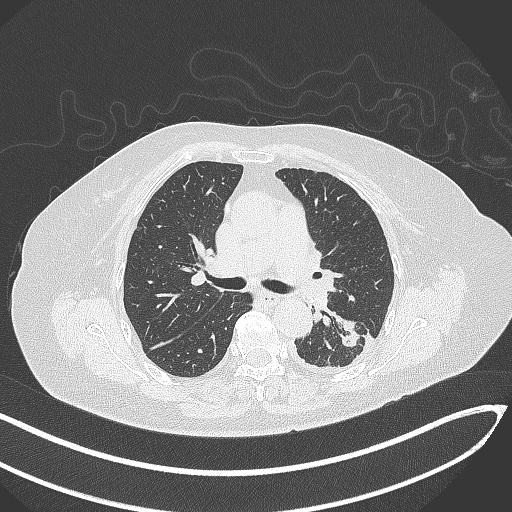
Chest CT, one axial slice; position 194 of 270 along the scan axis; reconstruction kernel B70f; 120 kVp; lung window (W 1500 / L -600 HU); 1 mm slice thickness; 512 × 512 image matrix. Female patient, age 76 years. Case-level facts recorded for this patient, not image findings: clinical TNM (as recorded): T1c N0 M0.
Structures marked on this image (rectangle marked by the reading radiologist):
- lung tumour (recorded histology: adenocarcinoma): bounding box <337,316,362,351> (left, top, right, bottom; pixels)